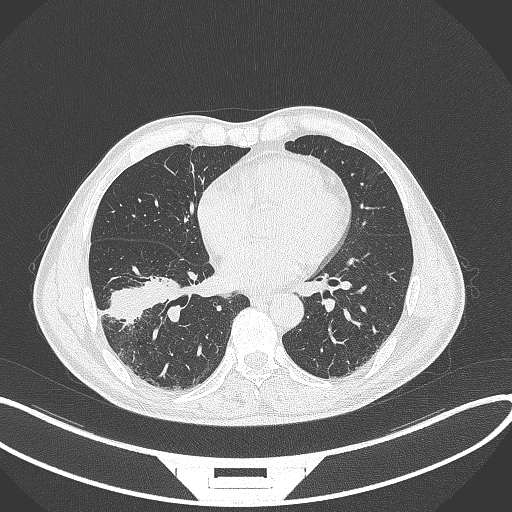
Chest CT, one axial slice; position 150 of 364 along the scan axis; reconstruction kernel B70f; 120 kVp; lung window (W 1500 / L -600 HU); 1 mm slice thickness; 512 × 512 image matrix, field of view 400 × 400 mm. Patient: male, 58 years. From the clinical record (not read from this slice): clinical TNM (as recorded): T3 N0 M0; histopathological grade: G2.
Outlined on this slice (rectangle marked by the reading radiologist):
- lung tumour (recorded histology: squamous cell carcinoma): bounding box <106,268,184,321> (left, top, right, bottom; pixels)